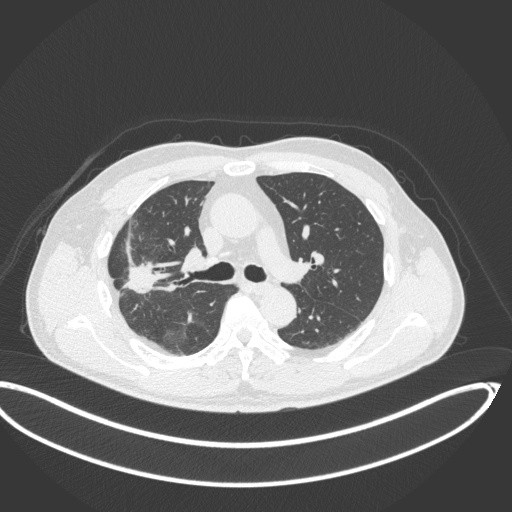
Chest CT, one axial slice. Position 218 of 341 along the scan axis. Reconstruction kernel B31f. Lung window (W 1500 / L -600 HU). 1 mm slice thickness. 512 × 512 image matrix, field of view 439 × 439 mm. Male patient, age 63 years. Case-level facts recorded for this patient, not image findings: clinical TNM (as recorded): T1c N0 M0.
Structures marked on this image (bounding box drawn by a radiologist):
- lung tumour (recorded histology: adenocarcinoma): bounding box (x1, y1, x2, y2) in pixels: (122, 254, 162, 300)